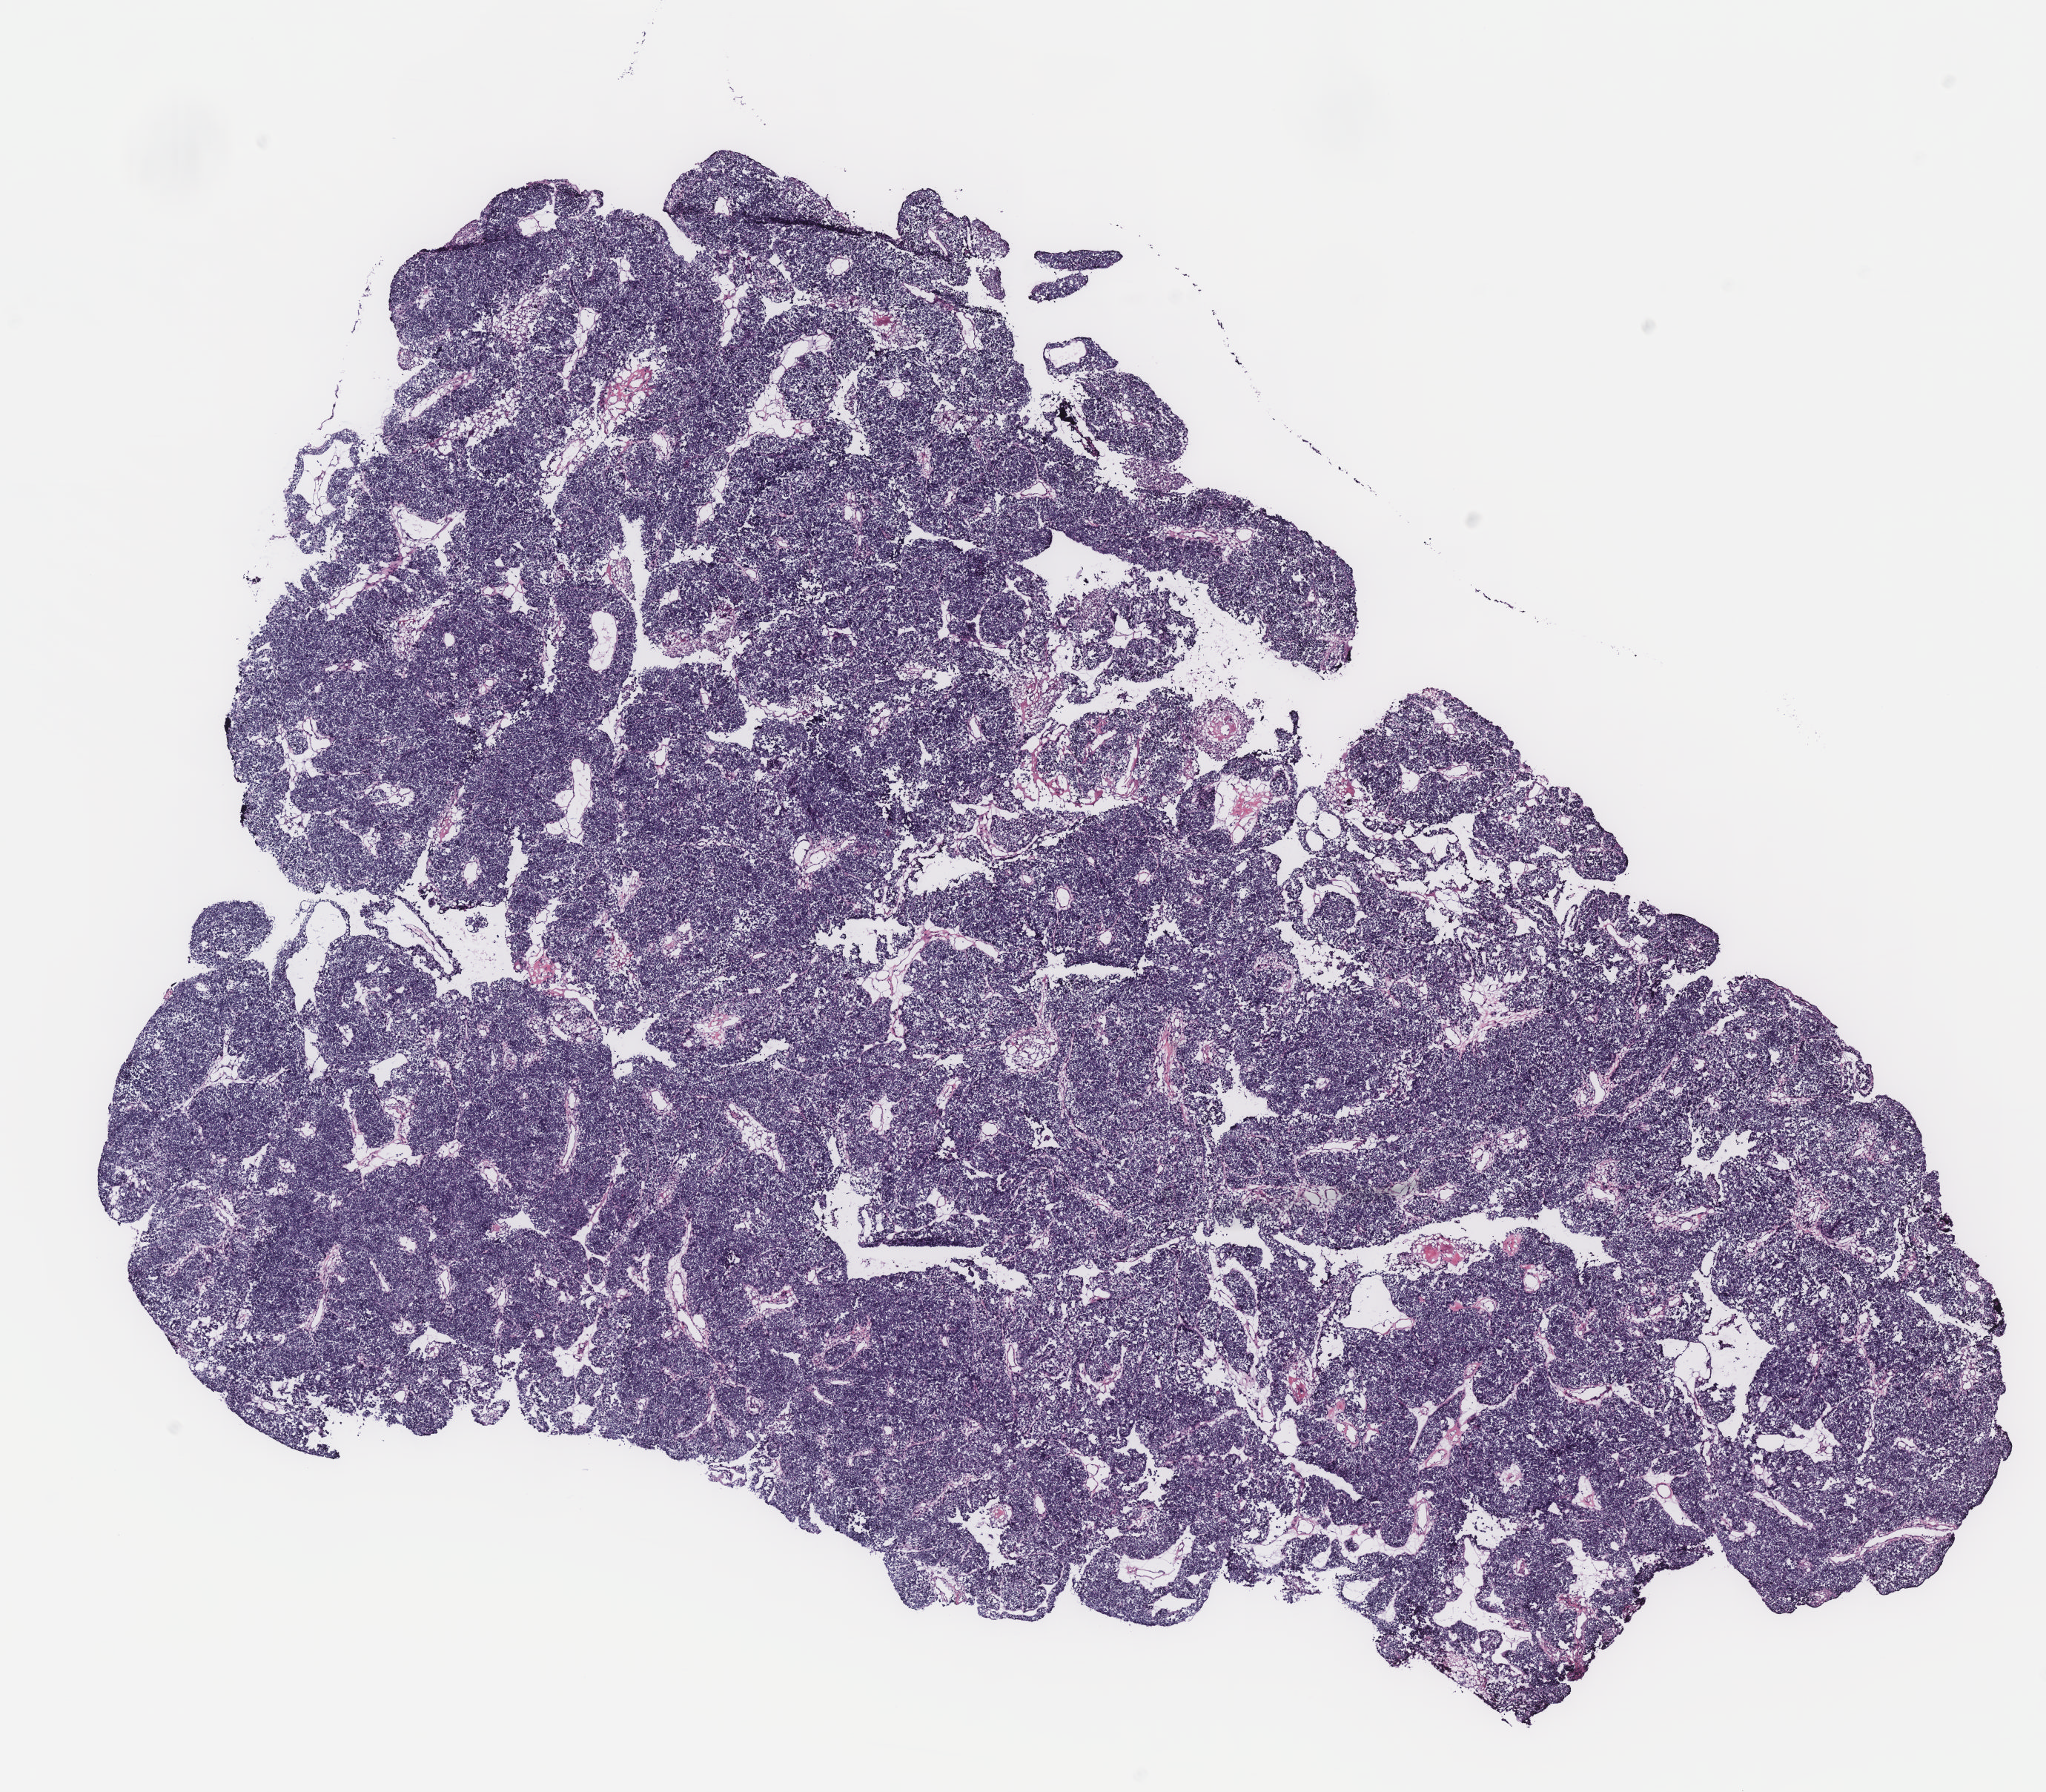
Hematoxylin and eosin (H&E) stained whole-slide image — a low-resolution overview of the entire scanned area, about 11.0 x 9.7 mm (slide scanned at 40x). Ovary, tissue type not recorded.
Patient diagnosis (cohort enrolment): ovarian cancer (ovary).